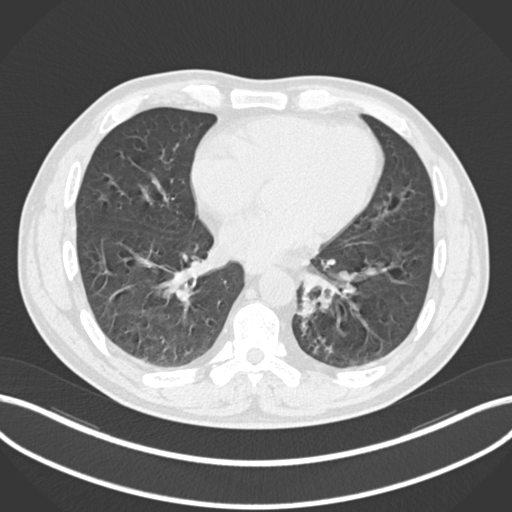
Chest CT, one axial slice. Lung window (W 1500 / L -600 HU). 1 mm slice thickness. 512 × 512 image matrix, field of view 400 × 400 mm. Patient: male, 50 years. From the clinical record (not read from this slice): clinical TNM (as recorded): T2a N3 M0.
Annotated regions visible in this slice (rectangle marked by the reading radiologist):
- lung tumour (recorded histology: squamous cell carcinoma): box from (x=294, y=293) to (x=321, y=322) px